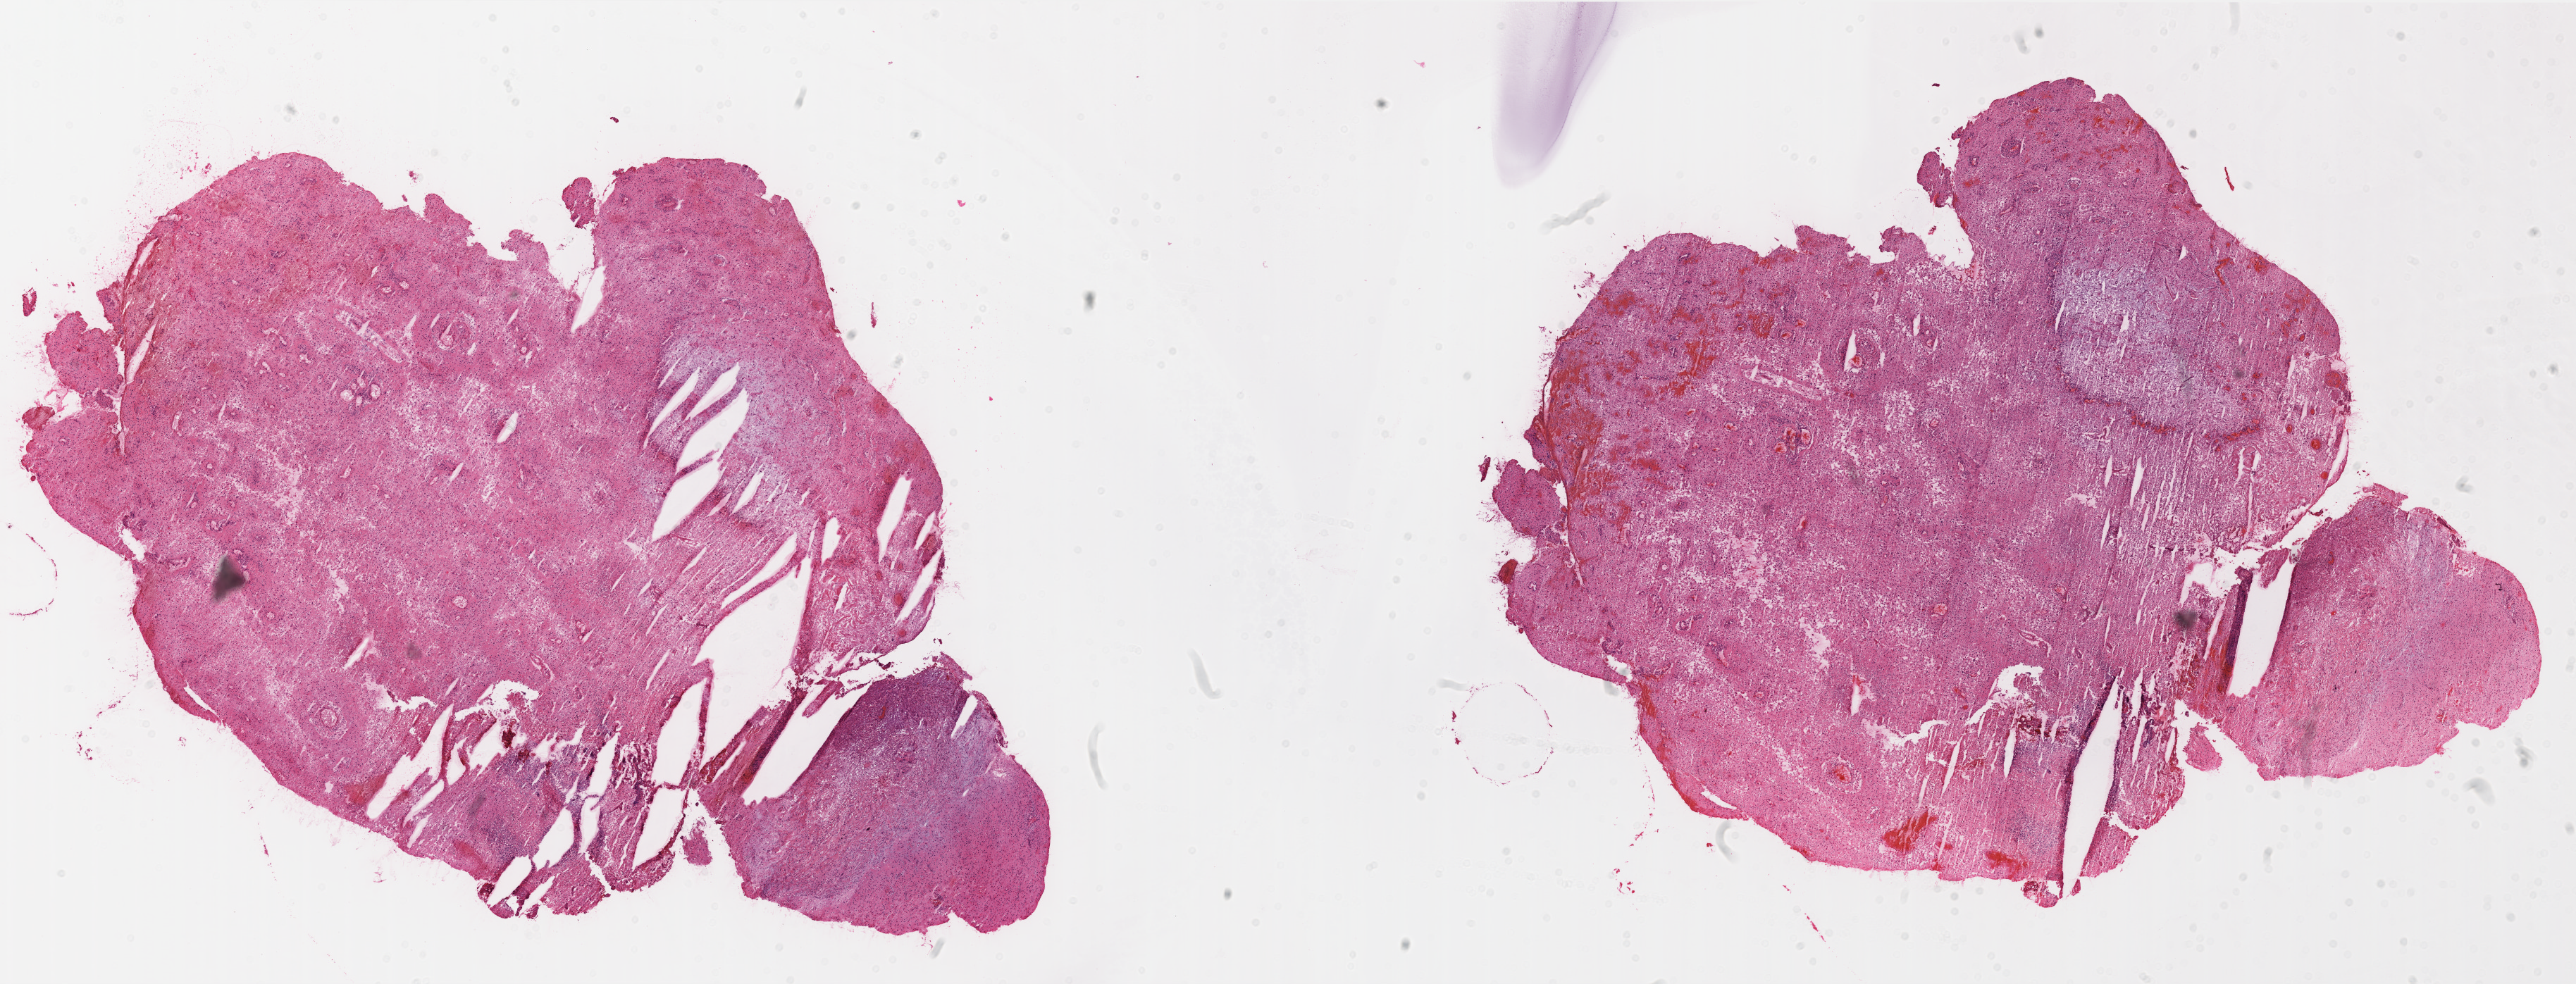
Whole-slide histology image, H&E, a low-resolution overview of the entire scanned area, about 29.4 x 11.2 mm (acquisition: 20x scan); frozen section from the top of the tissue portion; sample: primary tumour, brain. Male, age 56 years at initial diagnosis. Composition of this section per pathologist review: tumour cells 80%, tumour nuclei 90%, normal cells 0%, stromal cells 10%, necrosis 10%.
Histologic diagnosis: Glioblastoma.